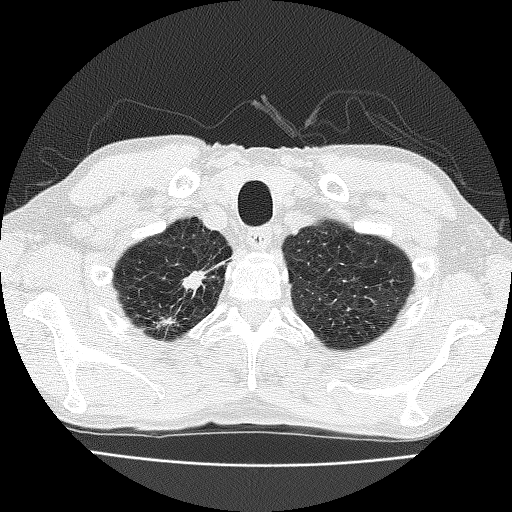
Low-dose screening chest CT, one axial slice; slice 158 of 185 in the series (ordered by position); reconstruction kernel FC51; lung window (W 1500 / L -600 HU); 512 × 512 image matrix, field of view 322 × 322 mm.
Structures marked on this image (expert manual segmentation):
- lesion 1 (nodule, upper lobe of right lung): bounding box (x1, y1, x2, y2) in pixels: (183, 271, 206, 291)
- lesion 2 (nodule, upper lobe of right lung): (157, 317, 175, 328)